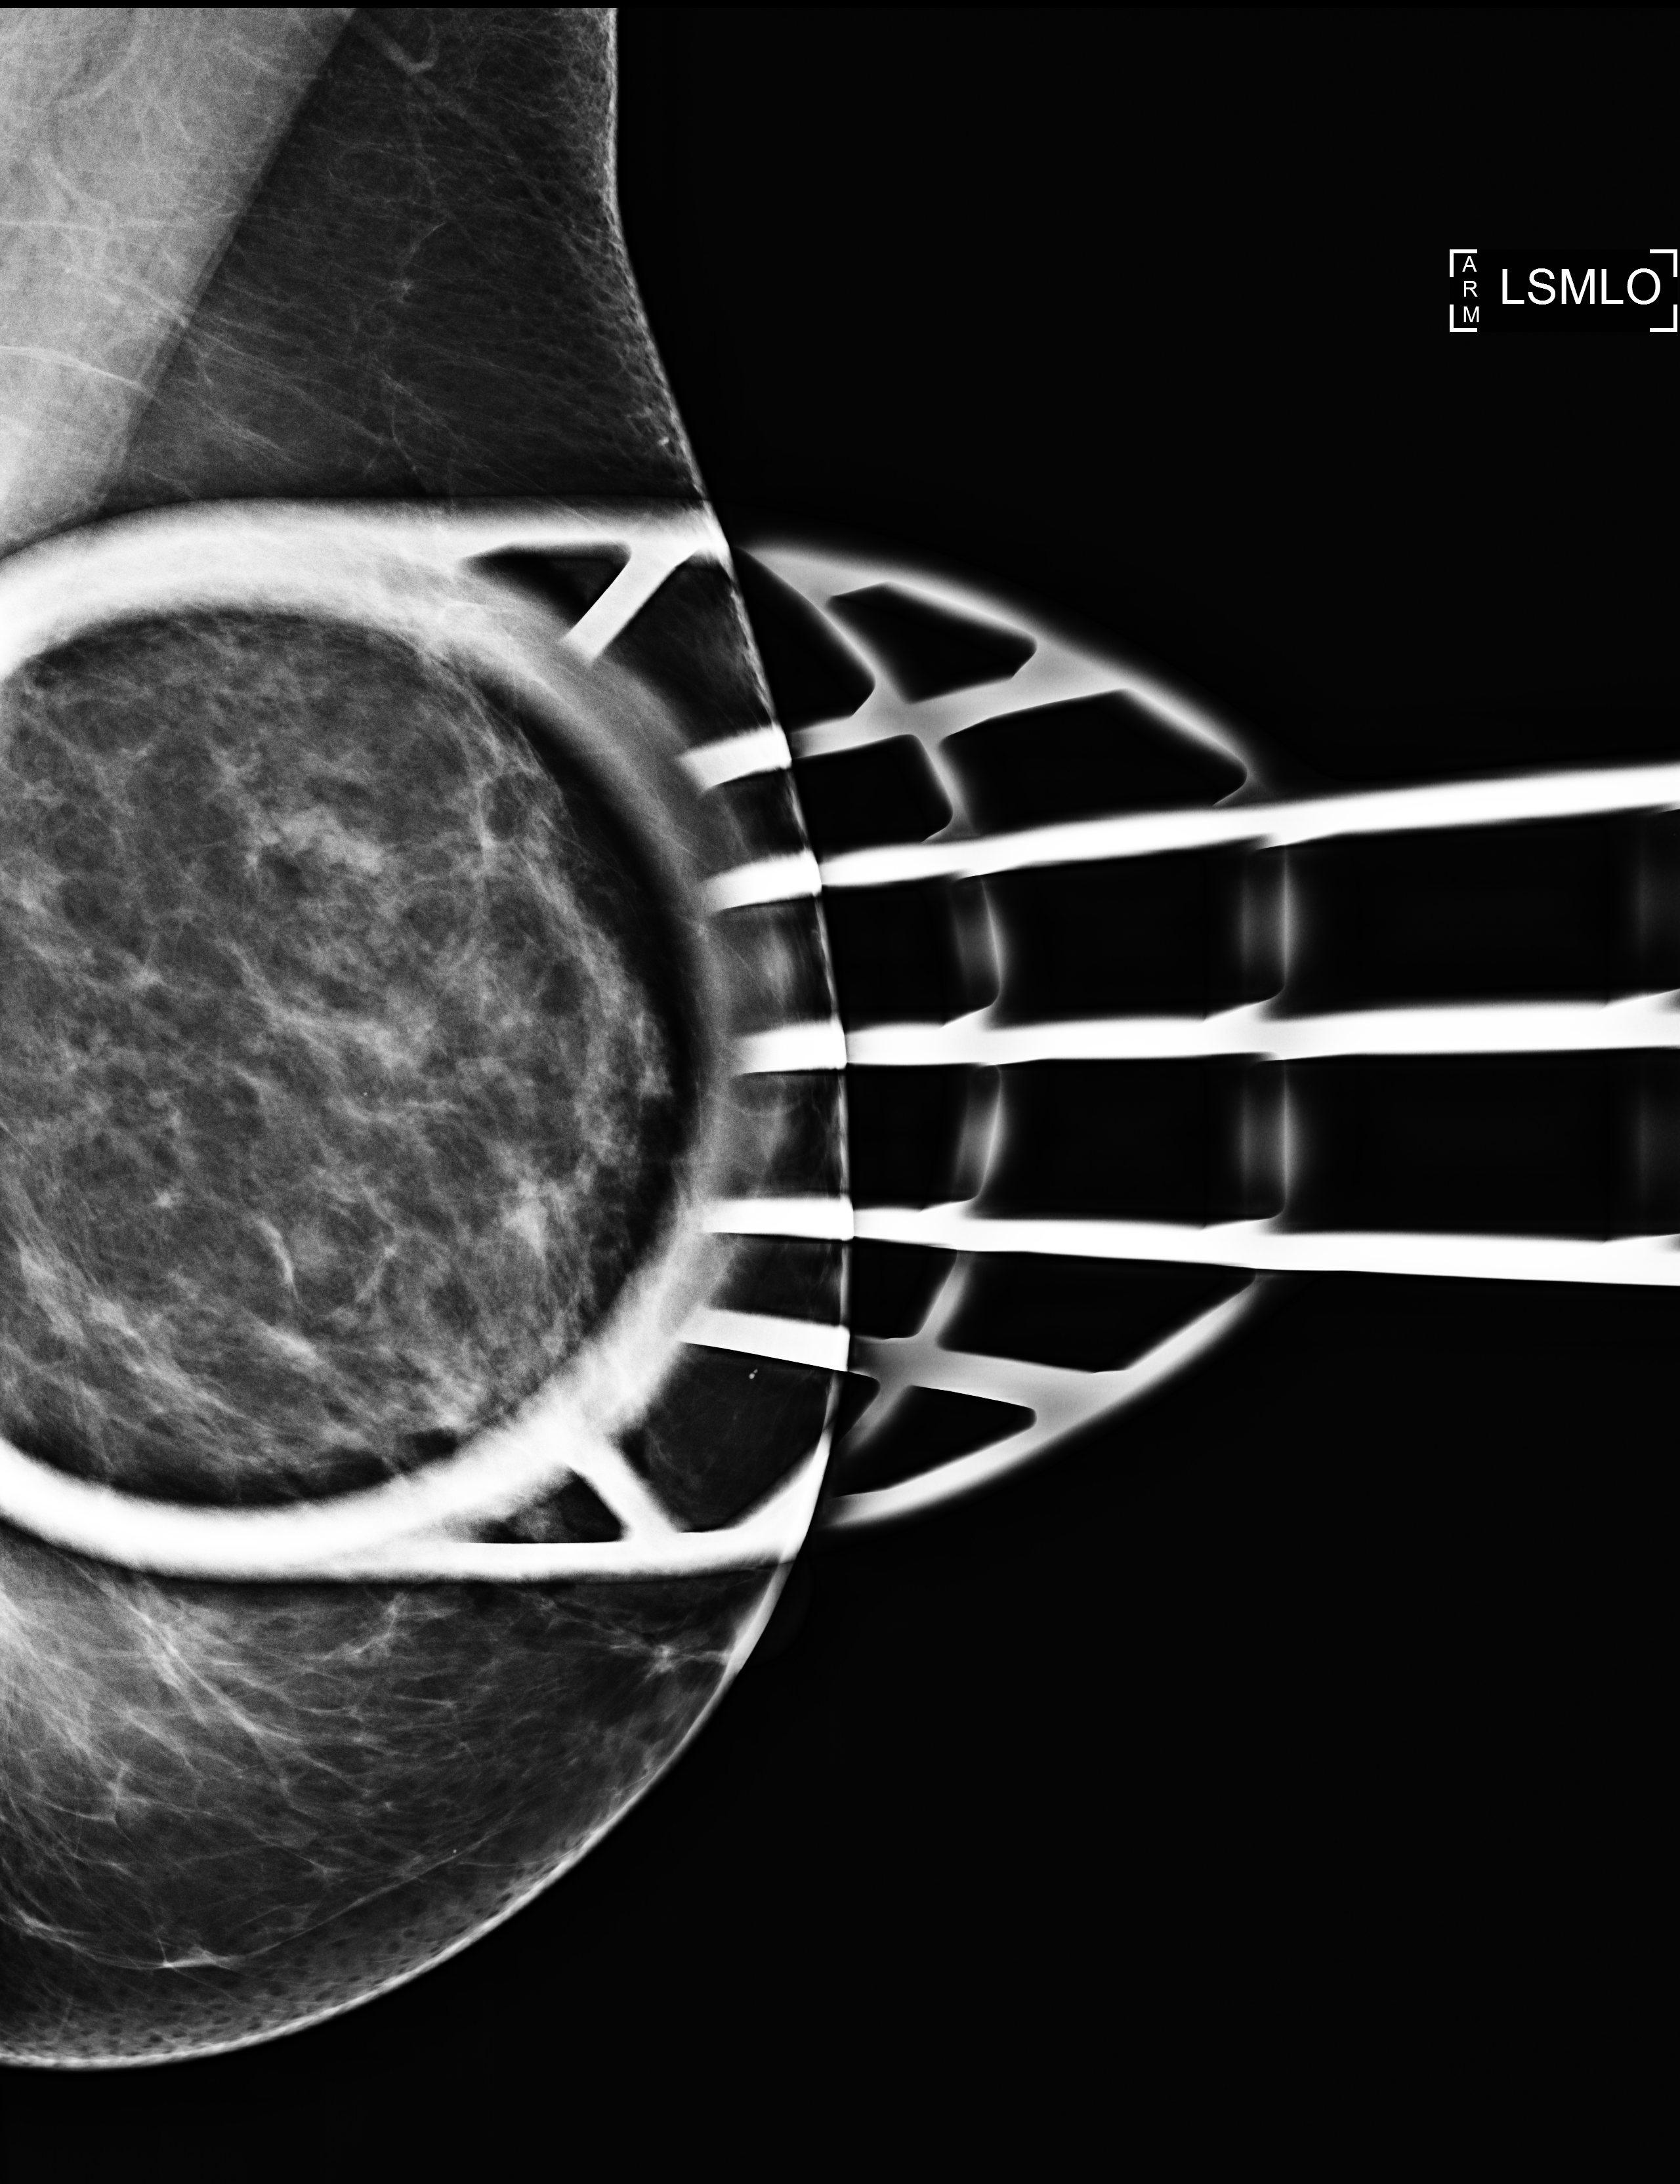
Additional work-up view, compressed breast thickness 78 mm, system: Selenia Dimensions.
Image type: full-field digital mammogram. Breast: left. Projection: mediolateral oblique (MLO) view, spot compression.